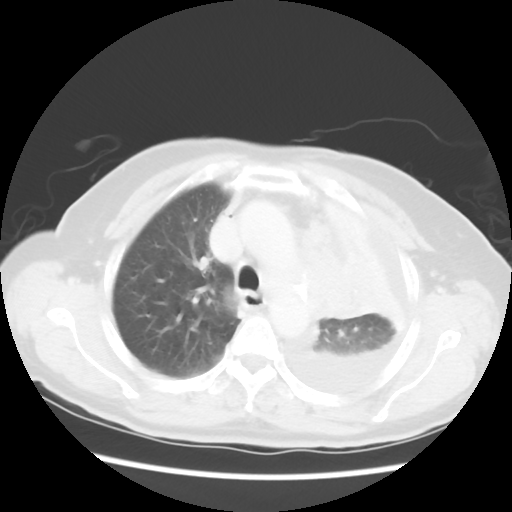
Chest CT, one axial slice. Reconstruction kernel STANDARD. Lung window (W 1500 / L -600 HU). 5 mm slice thickness. 512 × 512 image matrix. Female patient, age 72 years. From the clinical record (not read from this slice): clinical TNM (as recorded): T4 N3 M1b; histopathological grade: G3.
Structures marked on this image (bounding box drawn by a radiologist):
- lung tumour (recorded histology: large cell carcinoma): box from (x=296, y=244) to (x=383, y=330) px